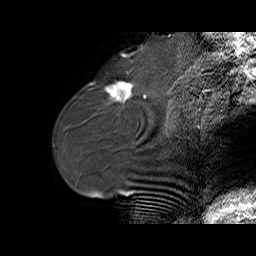
Breast MRI (dynamic contrast-enhanced), one sagittal slice; slice 21 of 70 in the series (ordered by position); dynamic contrast-enhanced series, time point 2 of 6 at this slice position (early post-contrast); 1.5 T; TE 5.5 ms, TR 32.9 ms; 256 × 256 image matrix, field of view 240 × 240 mm. Female patient. Case-level facts recorded for this patient, not image findings: setting: breast cancer imaged before/during neoadjuvant chemotherapy; receptor status: HER2-positive.
Outlined on this slice (semi-automatically segmented with operator editing):
- analysis volume of interest (the breast-tissue region the enhancement analysis was run in; not a lesion): box from (x=96, y=74) to (x=141, y=114) px
- tumour enhancement mask (voxels above the 100 % enhancement threshold inside the analysis volume of interest): (x=105, y=82)–(x=132, y=101)